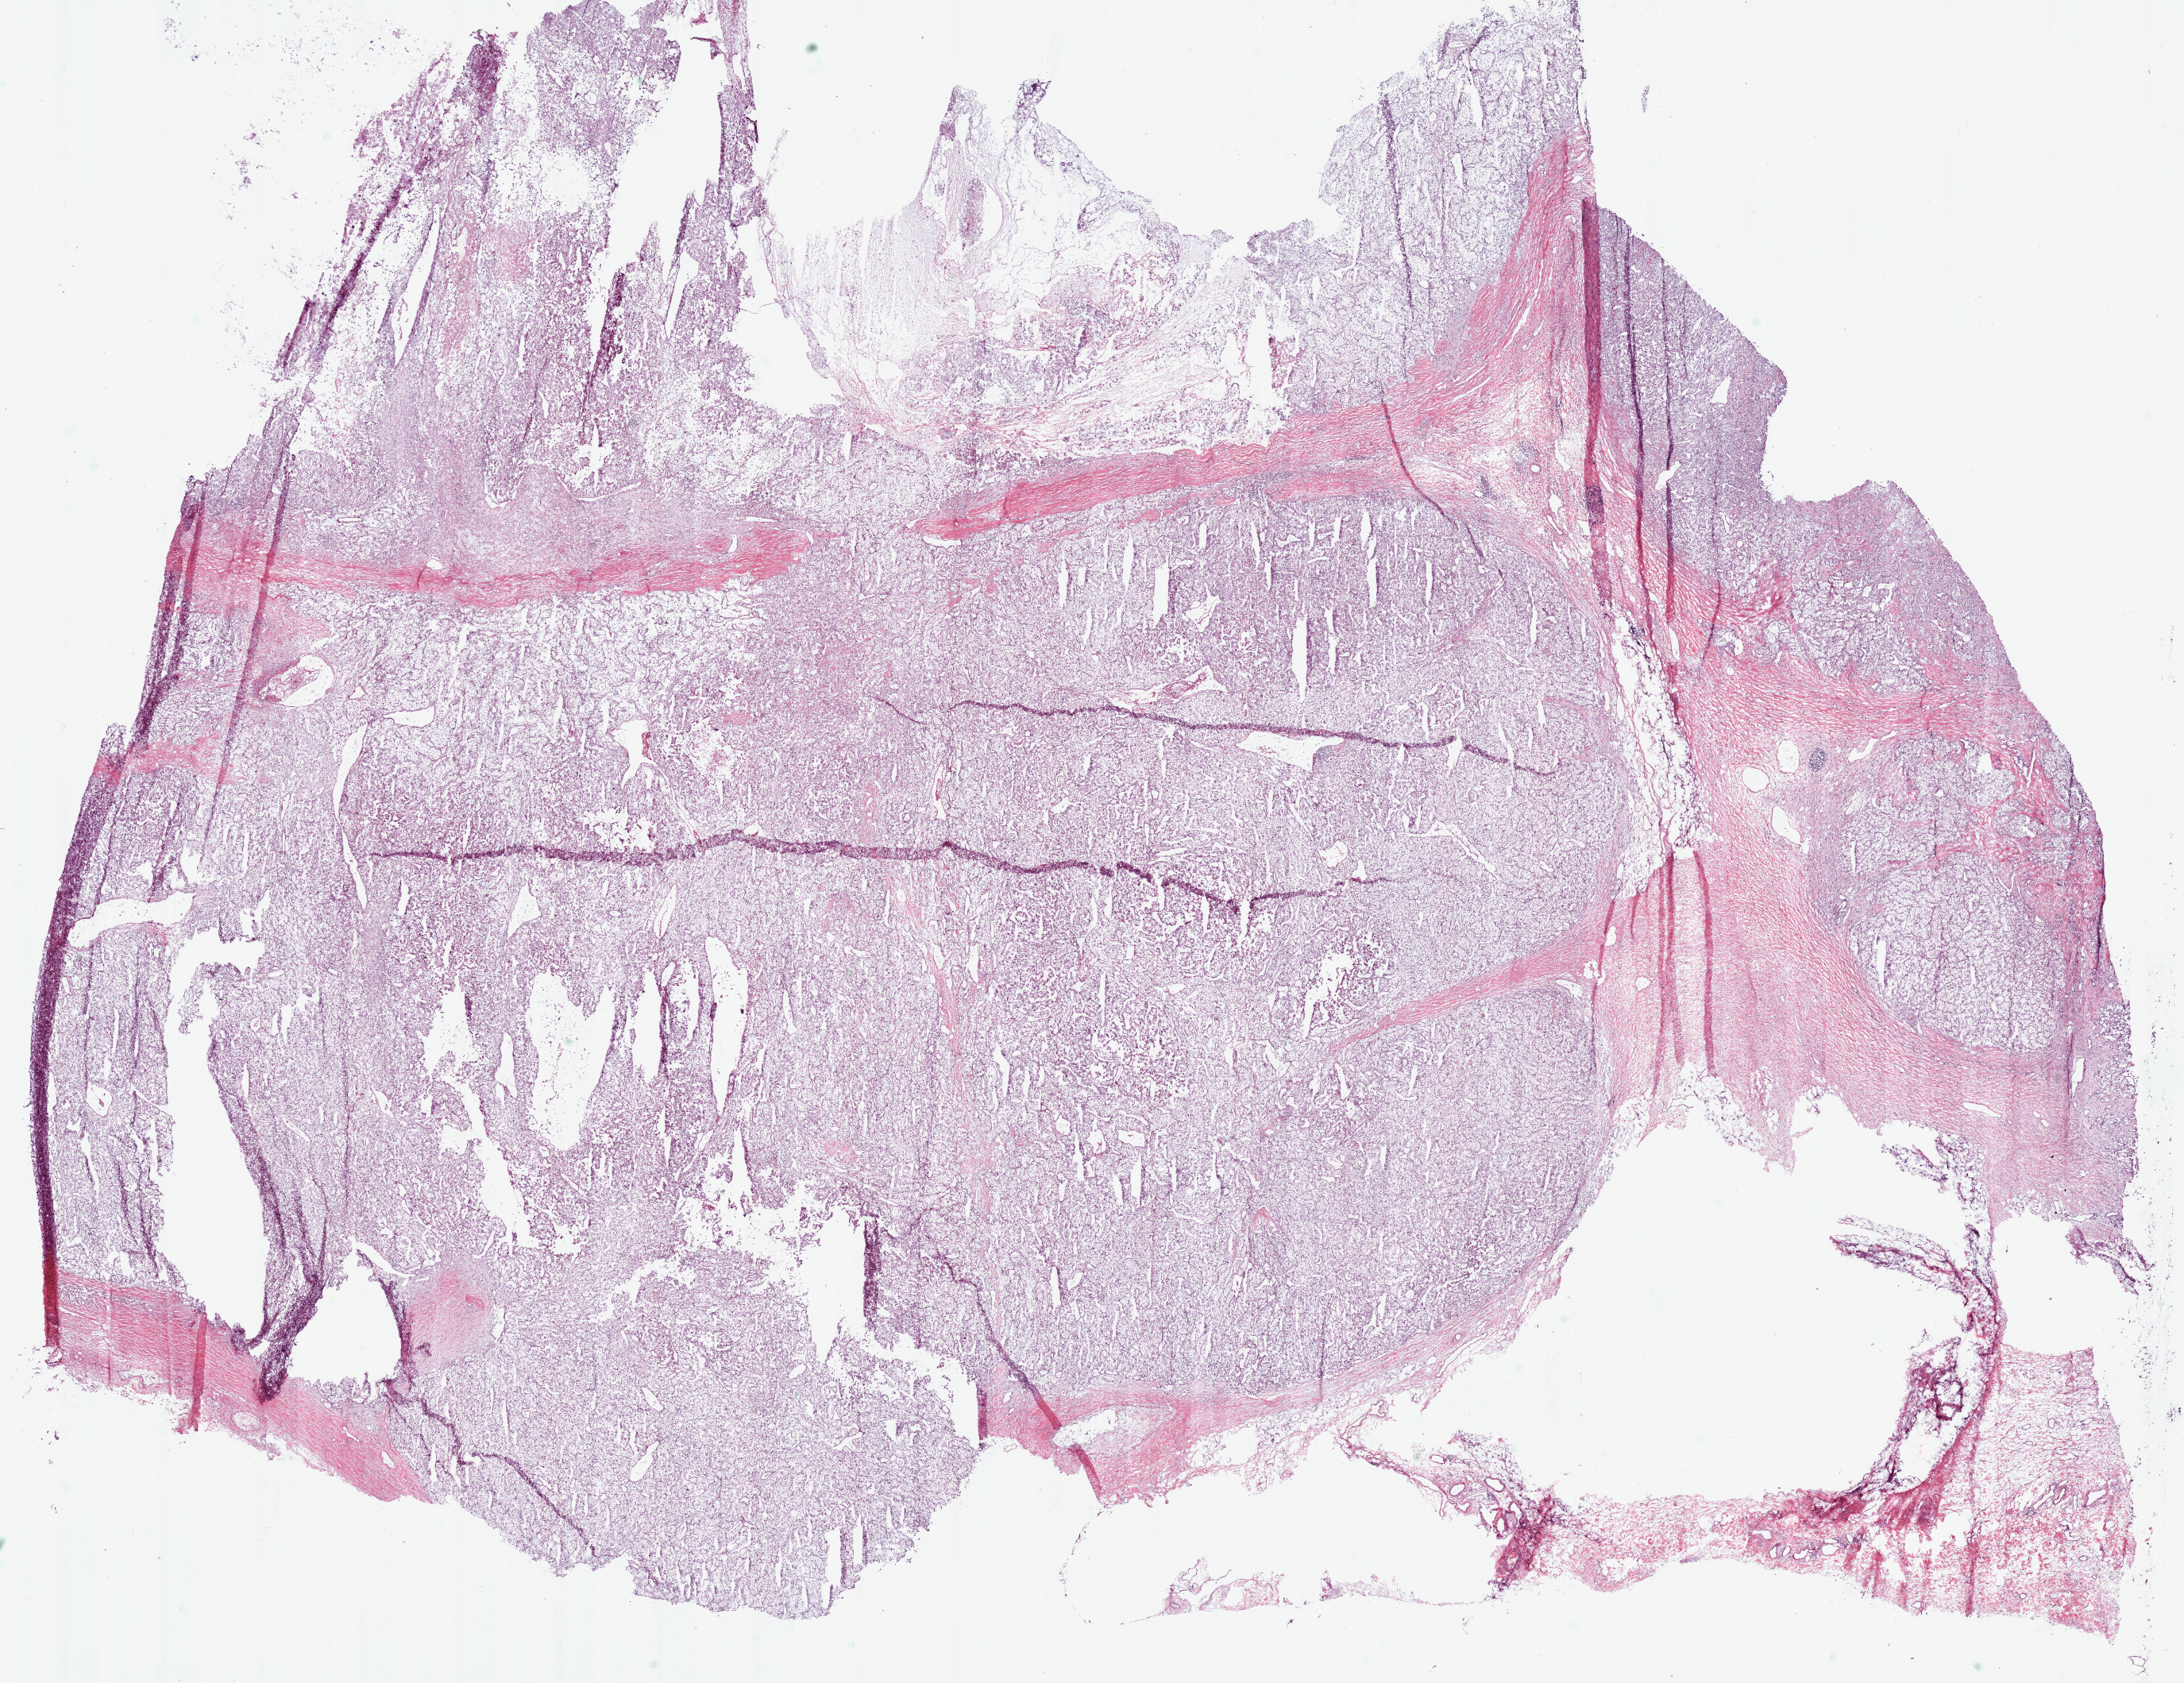
Whole-slide histology image, H&E-stained, shown as a low-resolution overview of the whole scanned area (about 22.1 x 17.0 mm, acquisition: 20x scan). Frozen section from the bottom of the tissue portion. Primary tumour sample from the kidney. Patient: female, age at initial diagnosis 59 years. Histologic grade: G4 (undifferentiated). Pathologist review of this section (percent, as recorded): tumour cells 80%, tumour nuclei 85%, normal cells 0%, stromal cells 10%, necrosis 10%.
AJCC pathologic stage: IV. Histologic diagnosis: Clear cell adenocarcinoma, NOS. Laterality: left. Lymph nodes positive (case pathology): 0 of 19 examined.